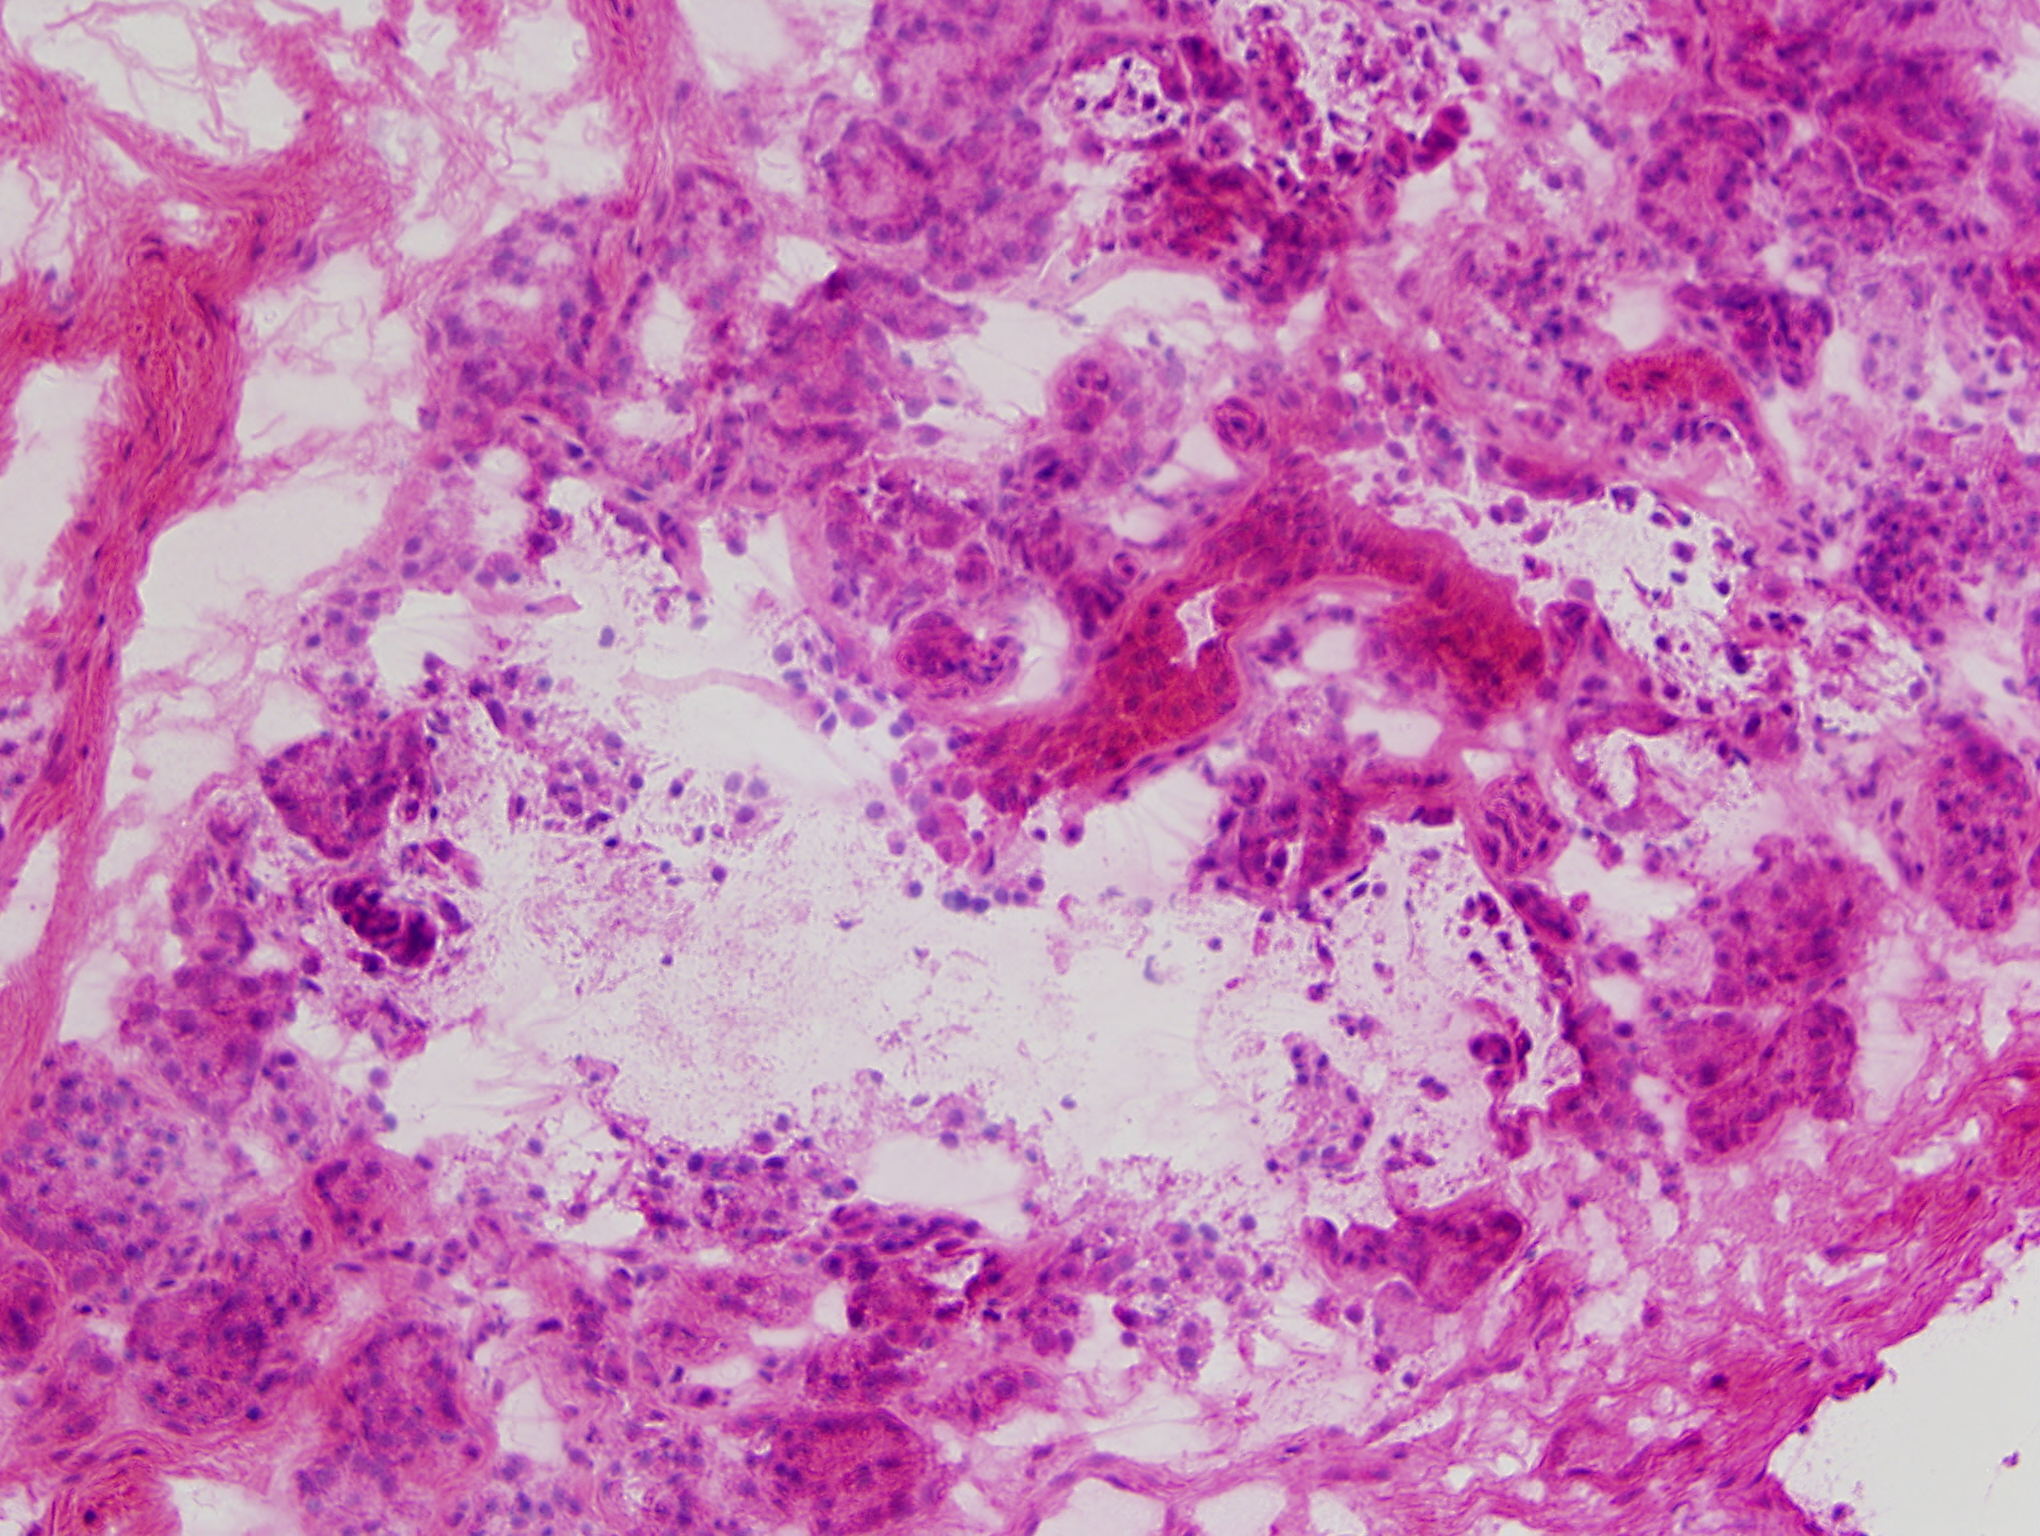
Single-field Hematoxylin and eosin (H&E) stained photomicrograph, roughly 1.0 x 0.8 mm in extent. Frozen section from the top of the tissue portion. Solid tissue normal (non-tumour tissue) sample from the head and neck. Male, age 47 years at initial diagnosis. Infiltration values recorded for this section: lymphocyte infiltration 3%, monocyte infiltration 3%, neutrophil infiltration 1%.
* this section: solid tissue normal (non-tumour) sample from the same patient
* patient diagnosis: Squamous cell carcinoma, NOS (overlapping lesion of lip, oral cavity and pharynx)